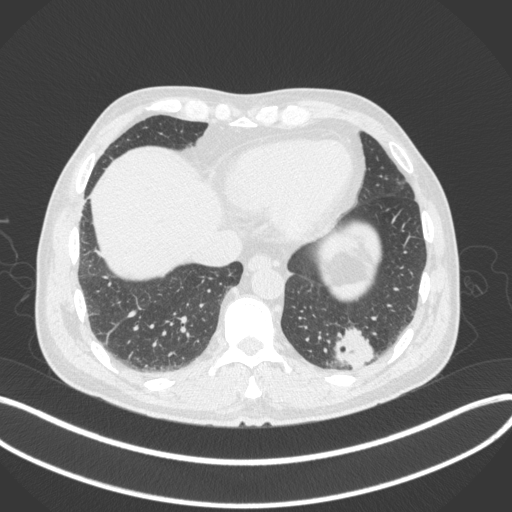
Chest CT, one axial slice; slice 66 of 313 in the series (ordered by position); reconstruction kernel B31f; lung window (W 1500 / L -600 HU); 512 × 512 image matrix, field of view 400 × 400 mm. Patient: male, 54 years. From the clinical record (not read from this slice): clinical TNM (as recorded): T1c N0 M1.
Annotated regions visible in this slice (rectangle marked by the reading radiologist):
- lung tumour (recorded histology: adenocarcinoma): box from (x=329, y=323) to (x=383, y=374) px